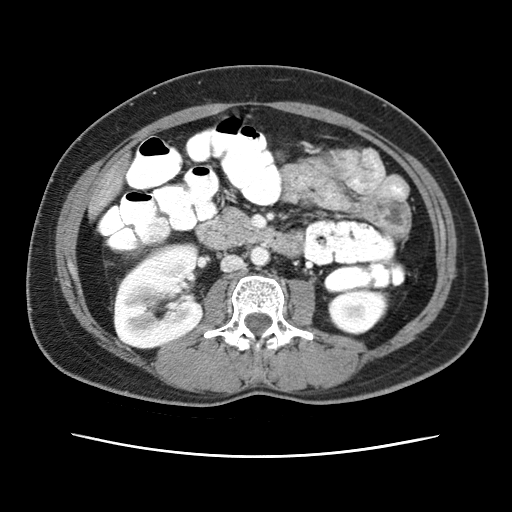
Contrast-enhanced abdominal CT (liver protocol), one axial slice; slice 5 of 79 in the series (ordered by position); reconstruction kernel STANDARD; 120 kVp; soft-tissue window (W 400 / L 40 HU); 2.5 mm slice thickness; 512 × 512 image matrix. Case-level facts recorded for this patient, not image findings: diagnosis: hepatocellular carcinoma (patient treated with transarterial chemoembolisation; whether this scan precedes or follows treatment is not stated here); TNM stage (as recorded): Stage-I.
Structures marked on this image (semi-automatically segmented with operator editing):
- abdominal aorta: bounding box (x1, y1, x2, y2) in pixels: (251, 248, 268, 267)
- liver parenchyma outside the tumour (the mass and vessels are separate outlines, so this box may not span the whole liver): (90, 162, 124, 214)